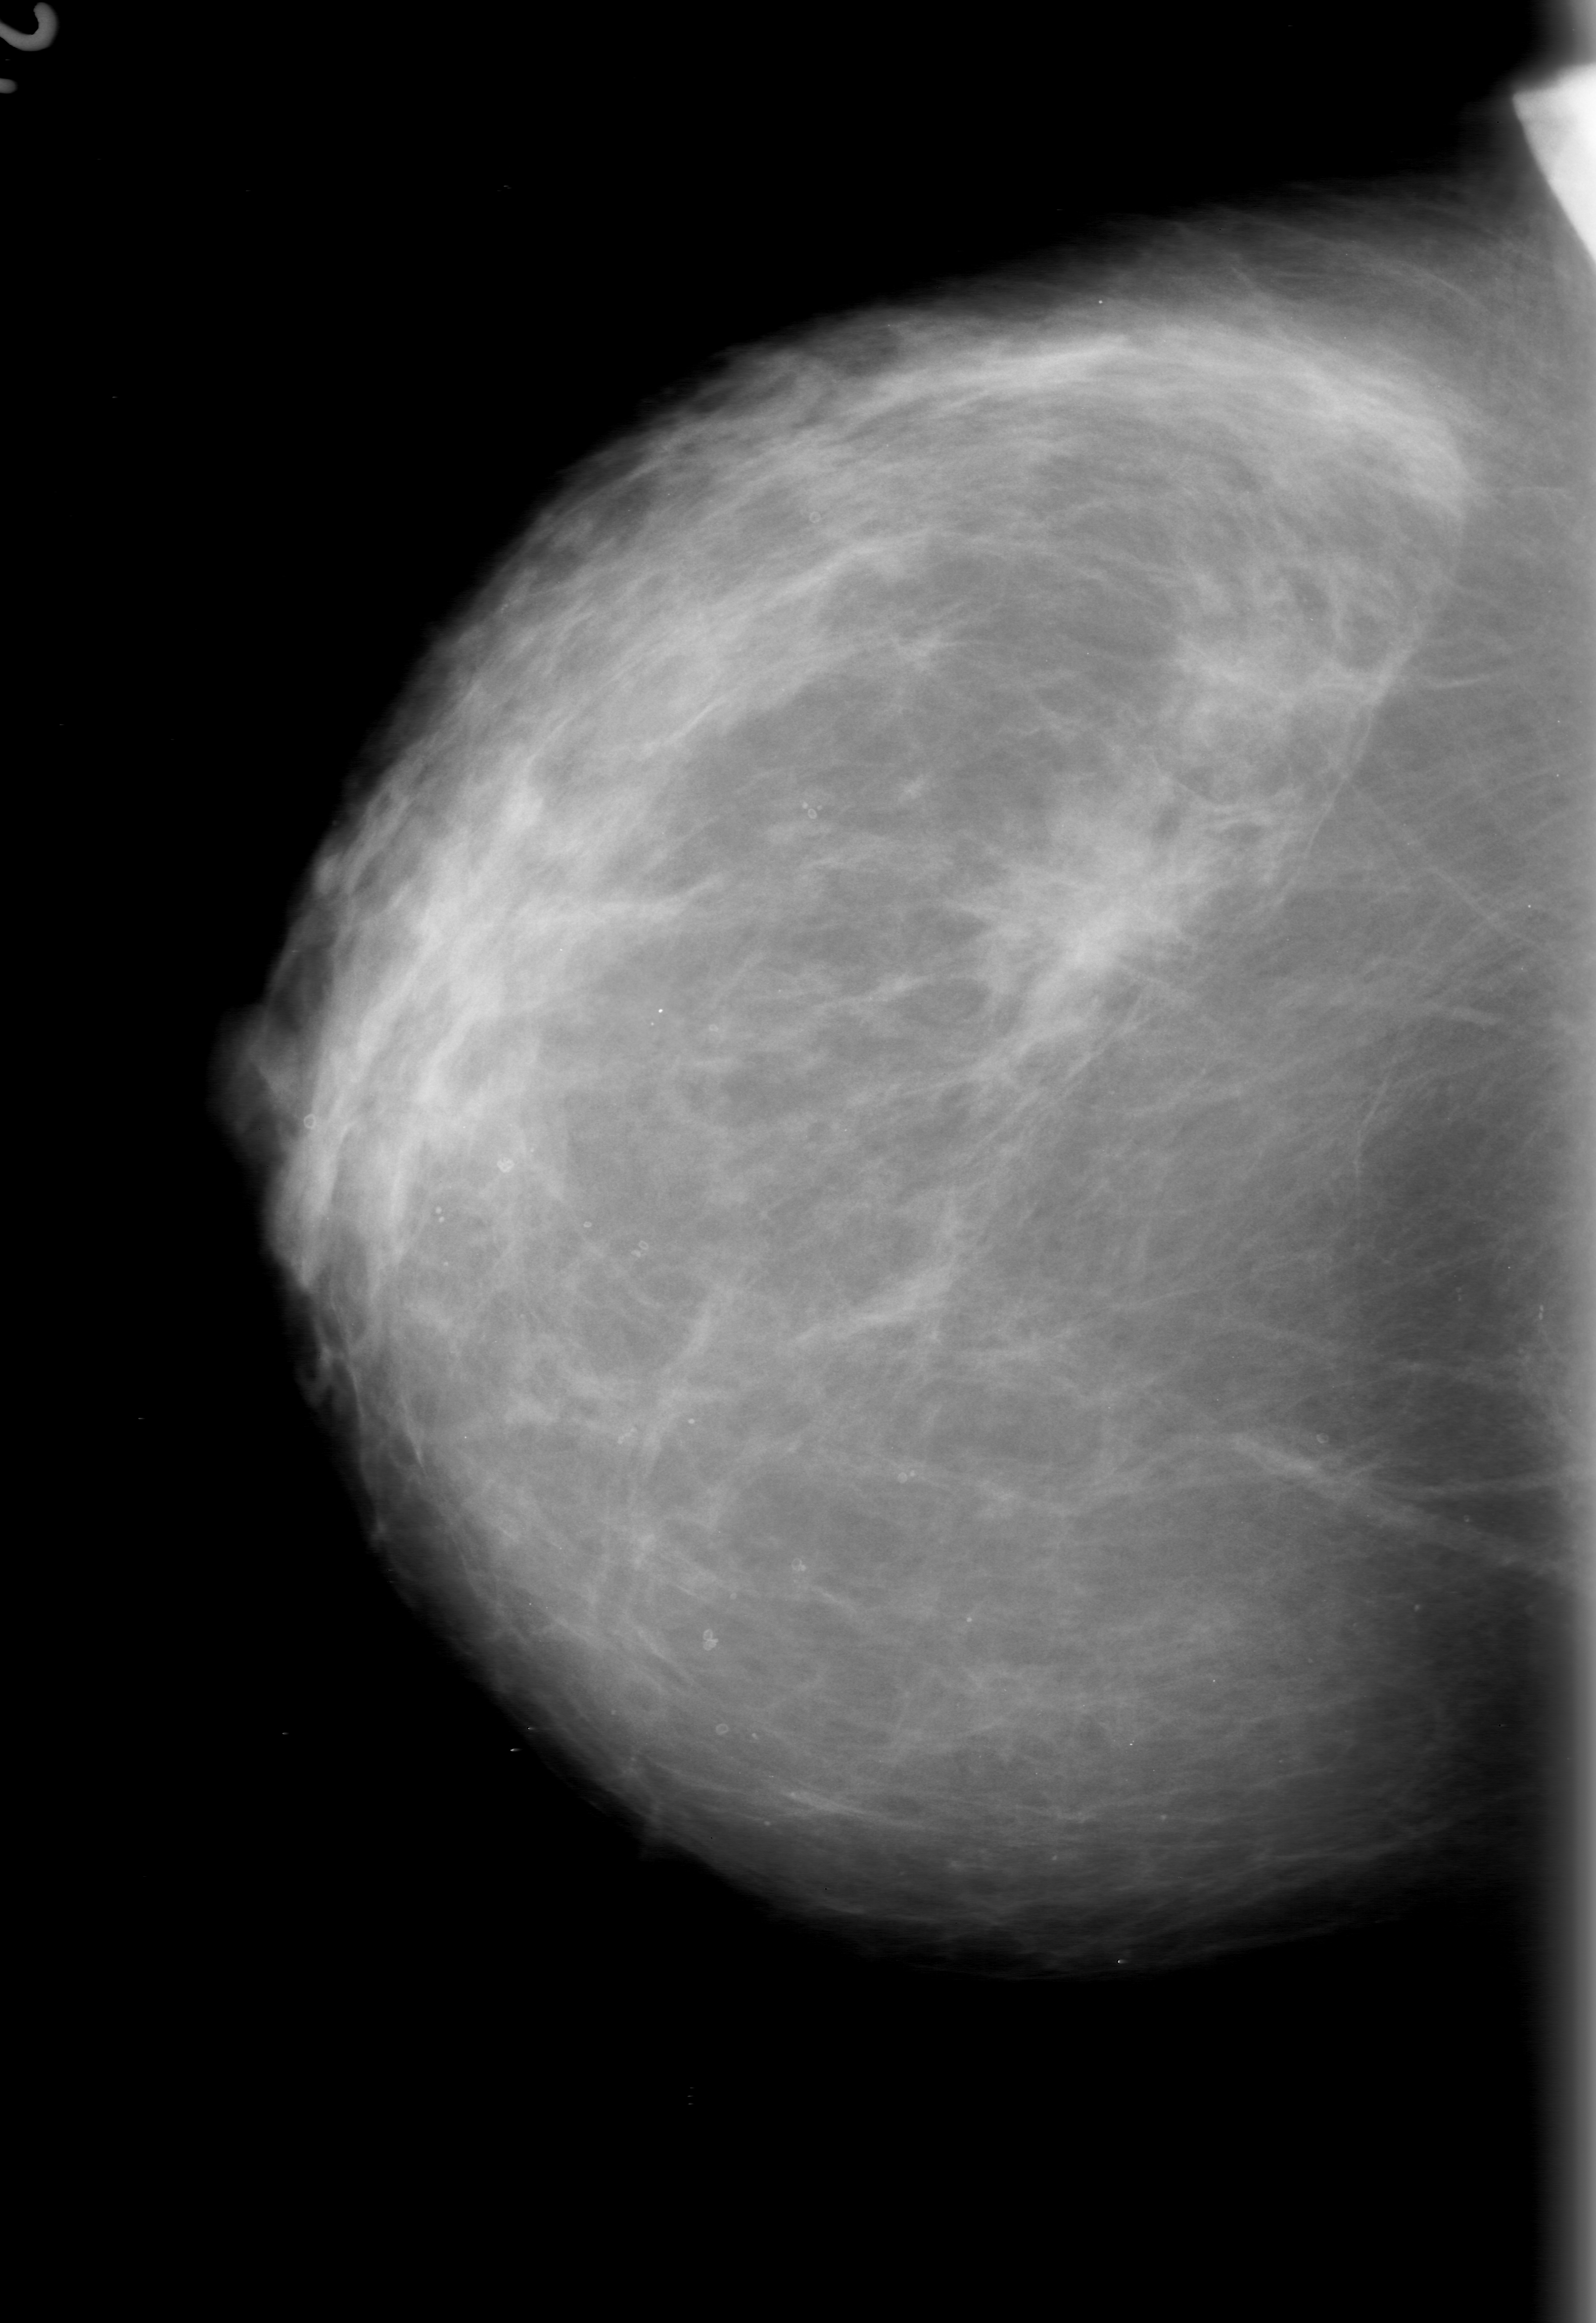
Mammogram (digitized film), right breast, CC view, BI-RADS breast density category 2 (scale 1–4).
- Radiologist-marked abnormalities on this image: mass, shape architectural distortion; BI-RADS assessment category 0 (incomplete: needs additional imaging); pathology (as recorded): malignant.